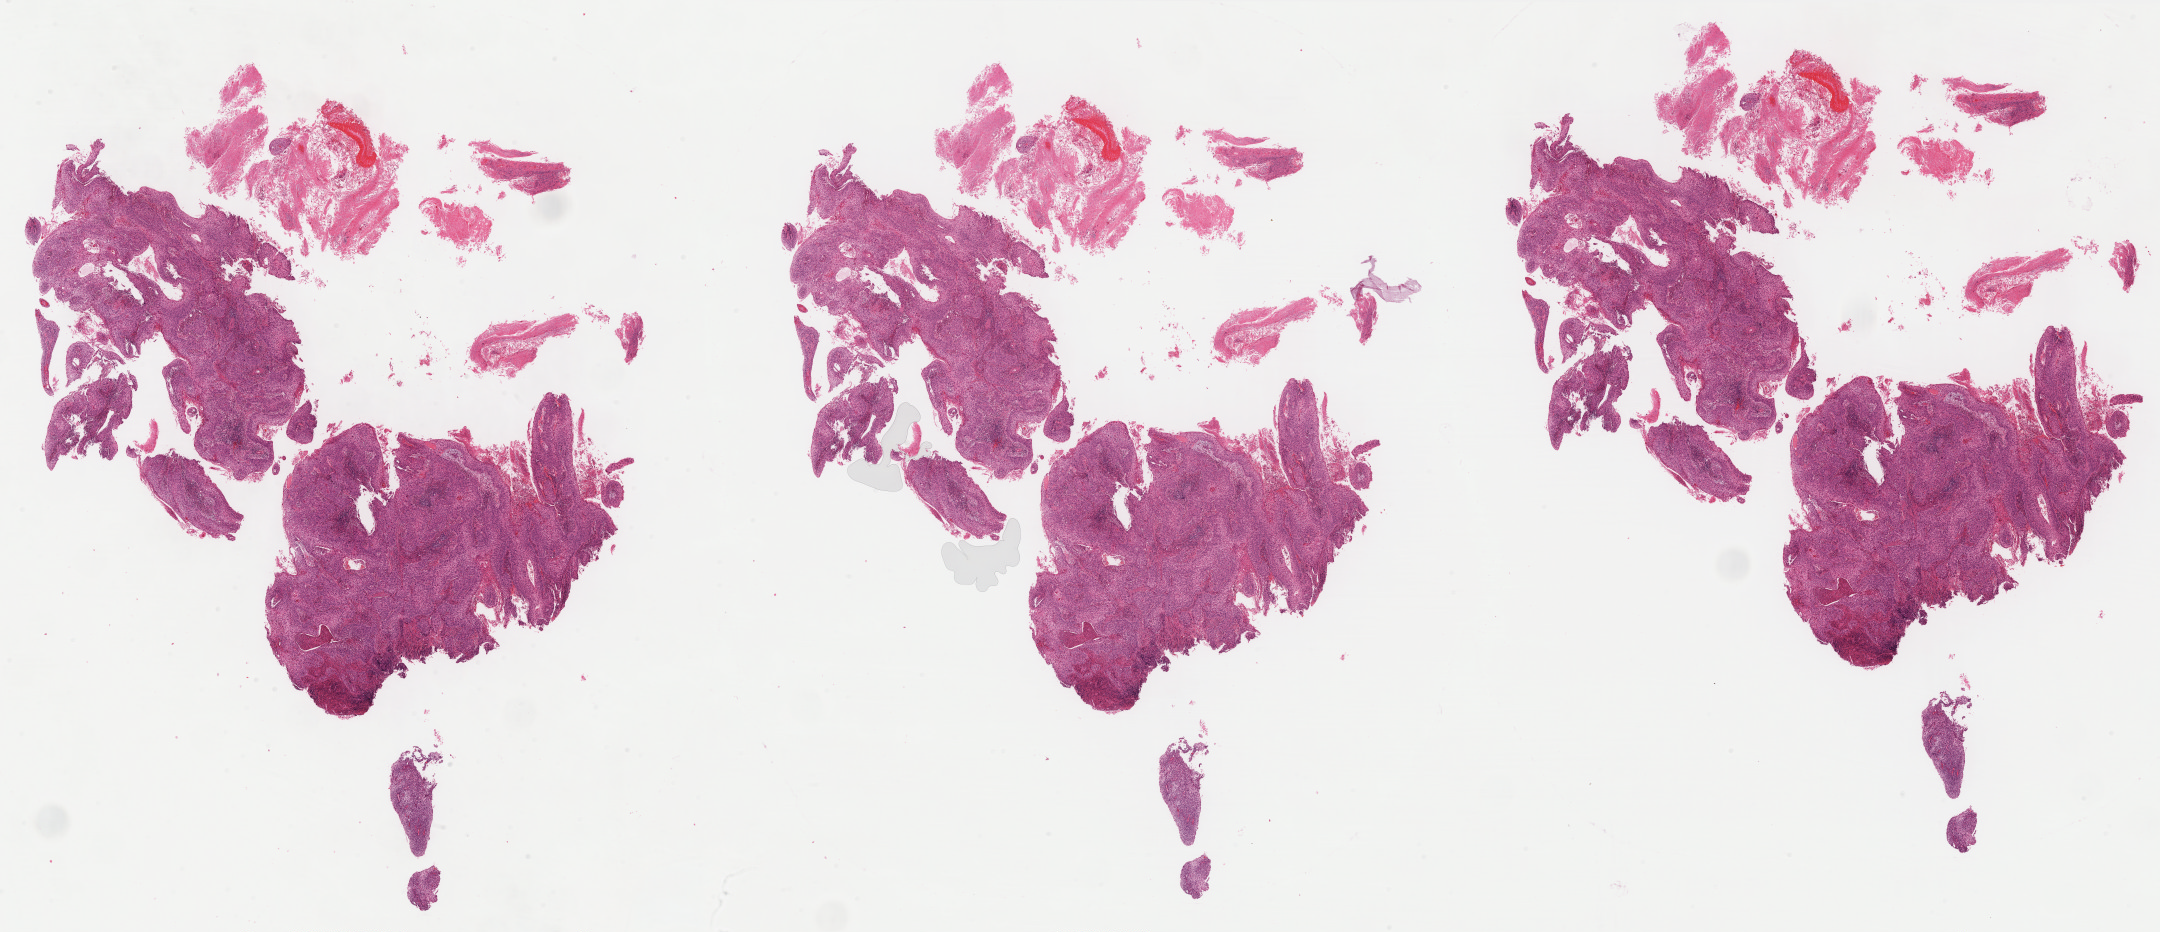
Whole-slide histology image, H&E-stained, whole scanned area (about 34.6 x 14.9 mm) shown as a low-resolution overview, formalin-fixed paraffin-embedded (FFPE) diagnostic section, primary tumour sample from the cervix. Female, age 46 years at initial diagnosis.
Histologic diagnosis: Squamous cell carcinoma, NOS (cervix uteri).